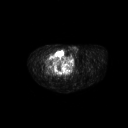
FDG PET of an extremity soft-tissue mass (from a PET/CT study), one axial slice. Slice 272 of 311 in the series (ordered by position). 128 × 128 image matrix, field of view 700 × 700 mm. Patient: male, 50 years. From the clinical record (not read from this slice): histological type: undifferentiated - pleiomorphic; grade: high; site of the primary tumour: right thigh.
Outlined on this slice (expert contour drawn on MRI and transferred to this co-registered scan by the dataset authors):
- gross tumour volume including surrounding oedema: bounding box <46,49,66,68> (left, top, right, bottom; pixels)
- gross tumour volume (mass): <46,49,66,68>